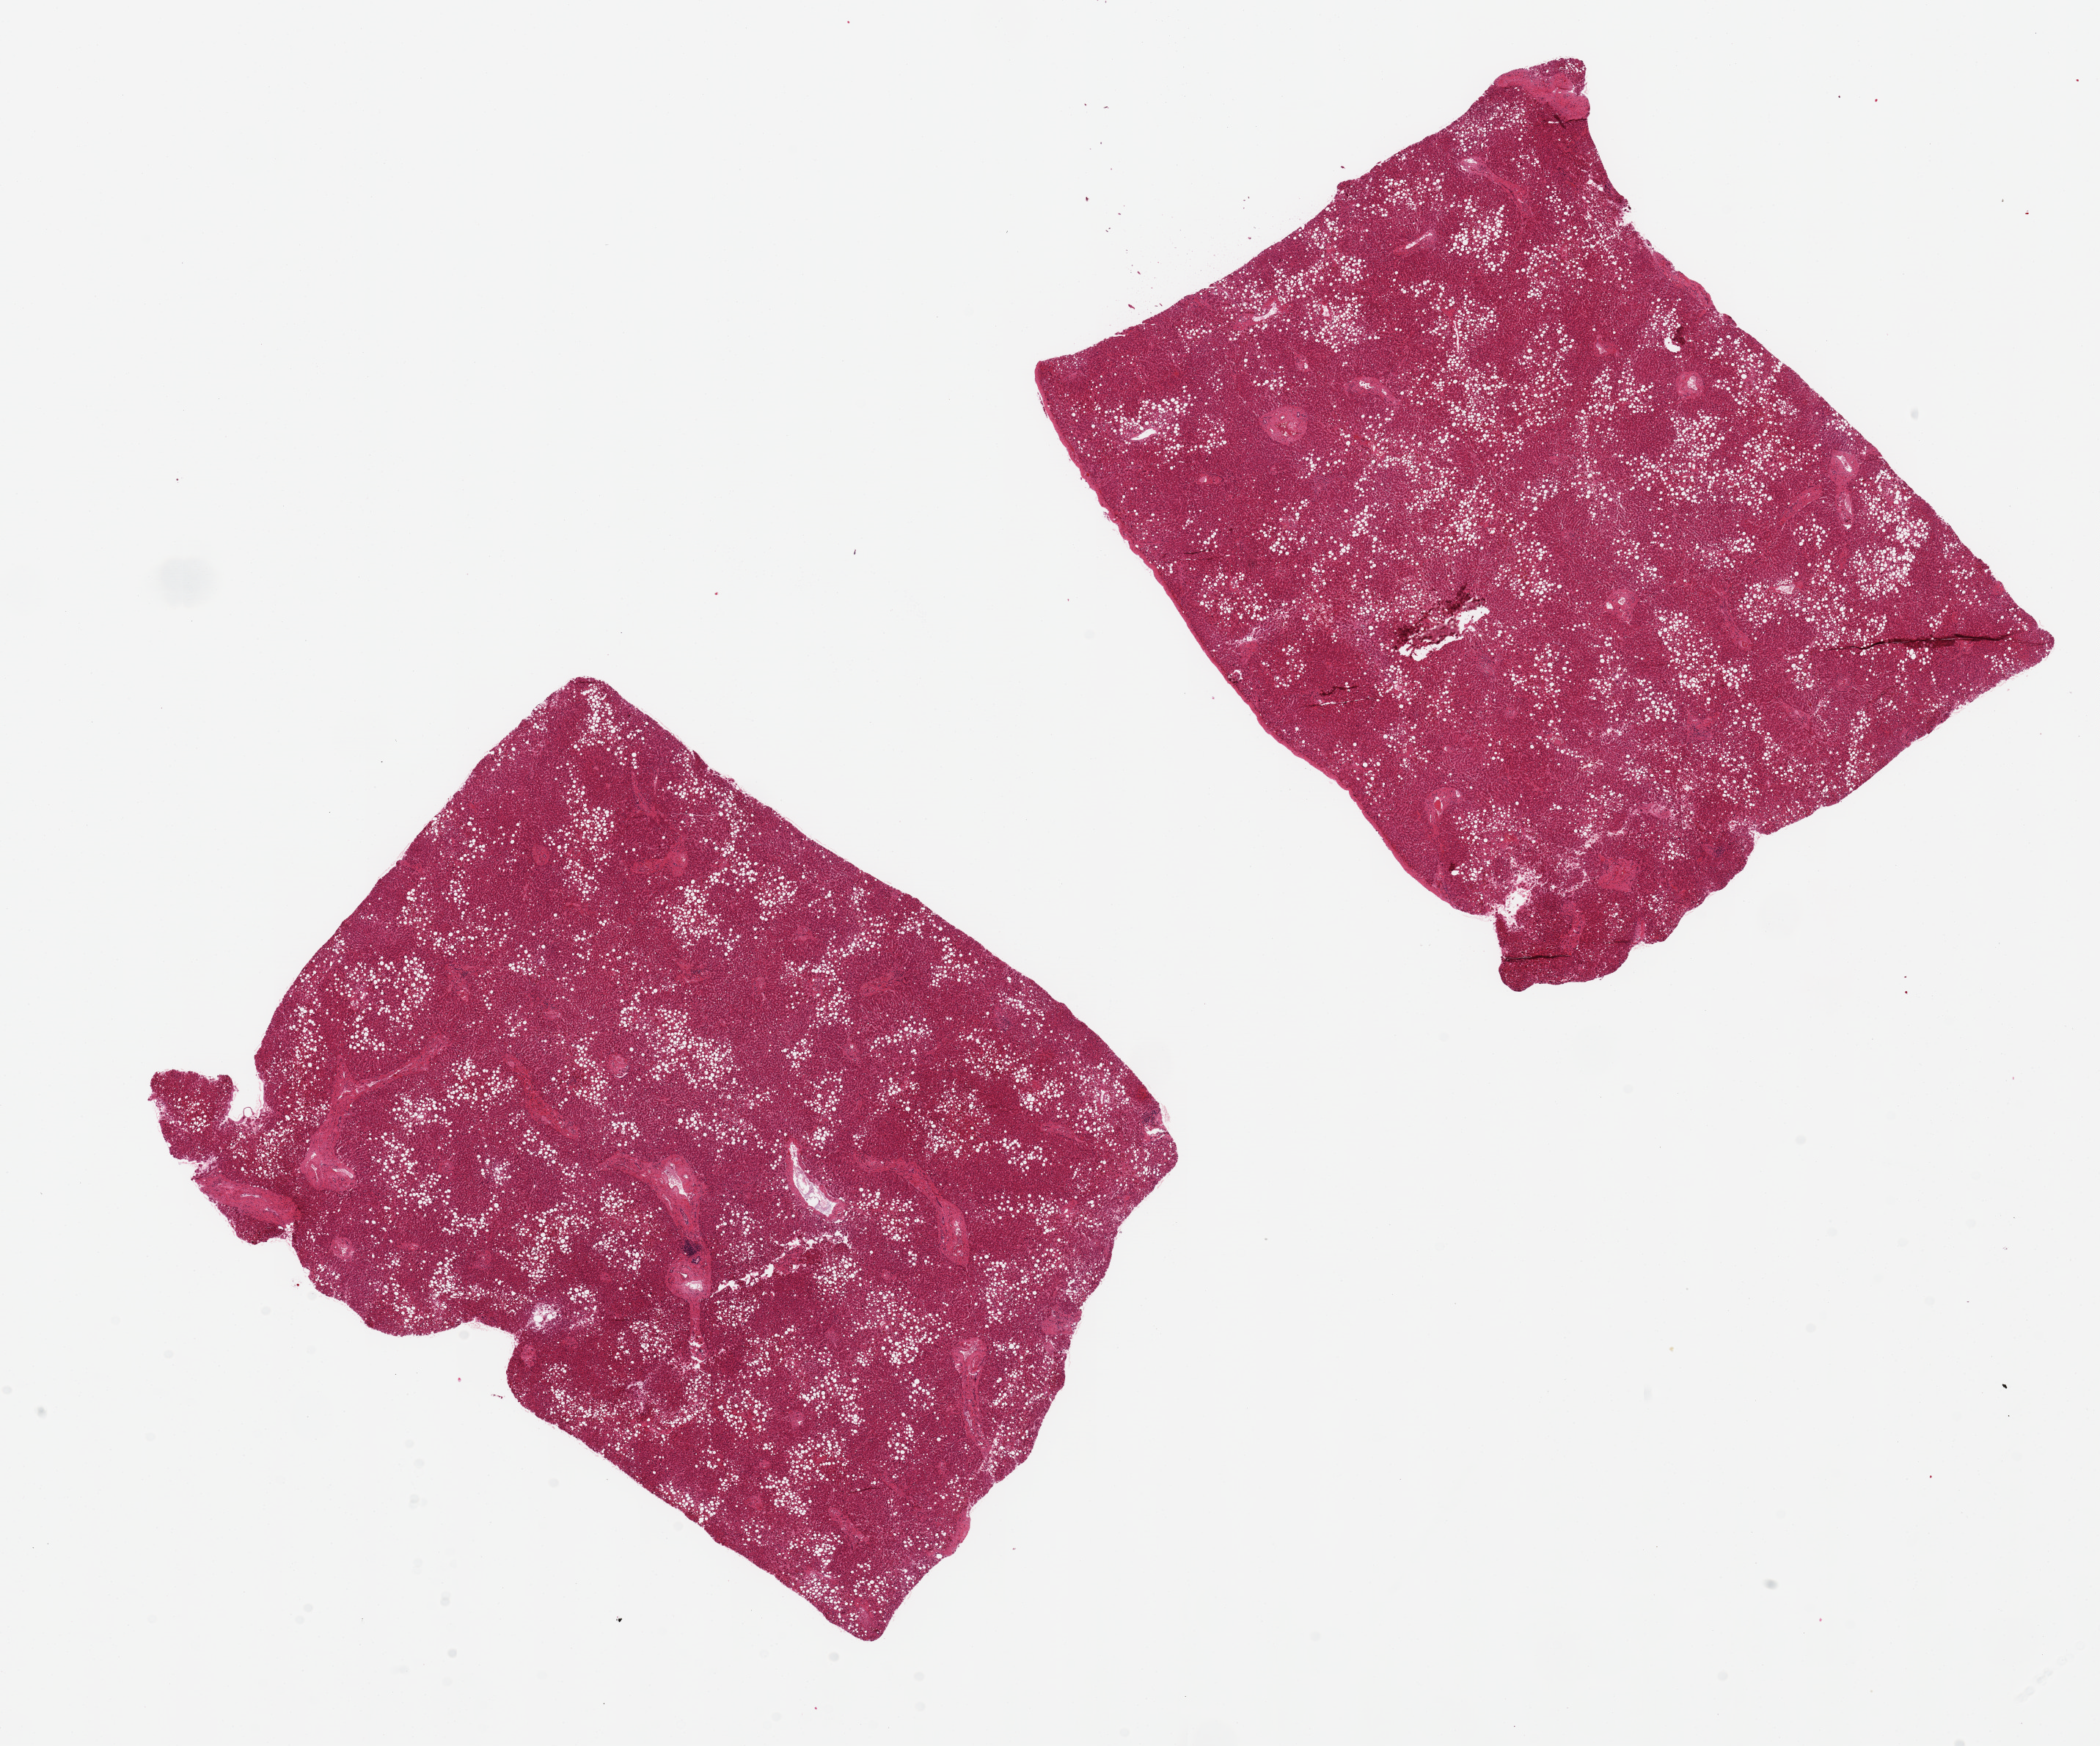
Digitized hematoxylin and eosin (H&E)-stained section — low-resolution overview of the scanned area, about 22.6 x 18.8 mm (slide scanned at 20x). PAXgene-fixed, paraffin-embedded tissue. Section of liver (target tissue). Tissue donor sample. Donor: male.
Pathologist's review note for this sample: 2 aliquots, ~8x7.5mm. Diffuse macrovesicular steatosis, ~50% of parenchyma.